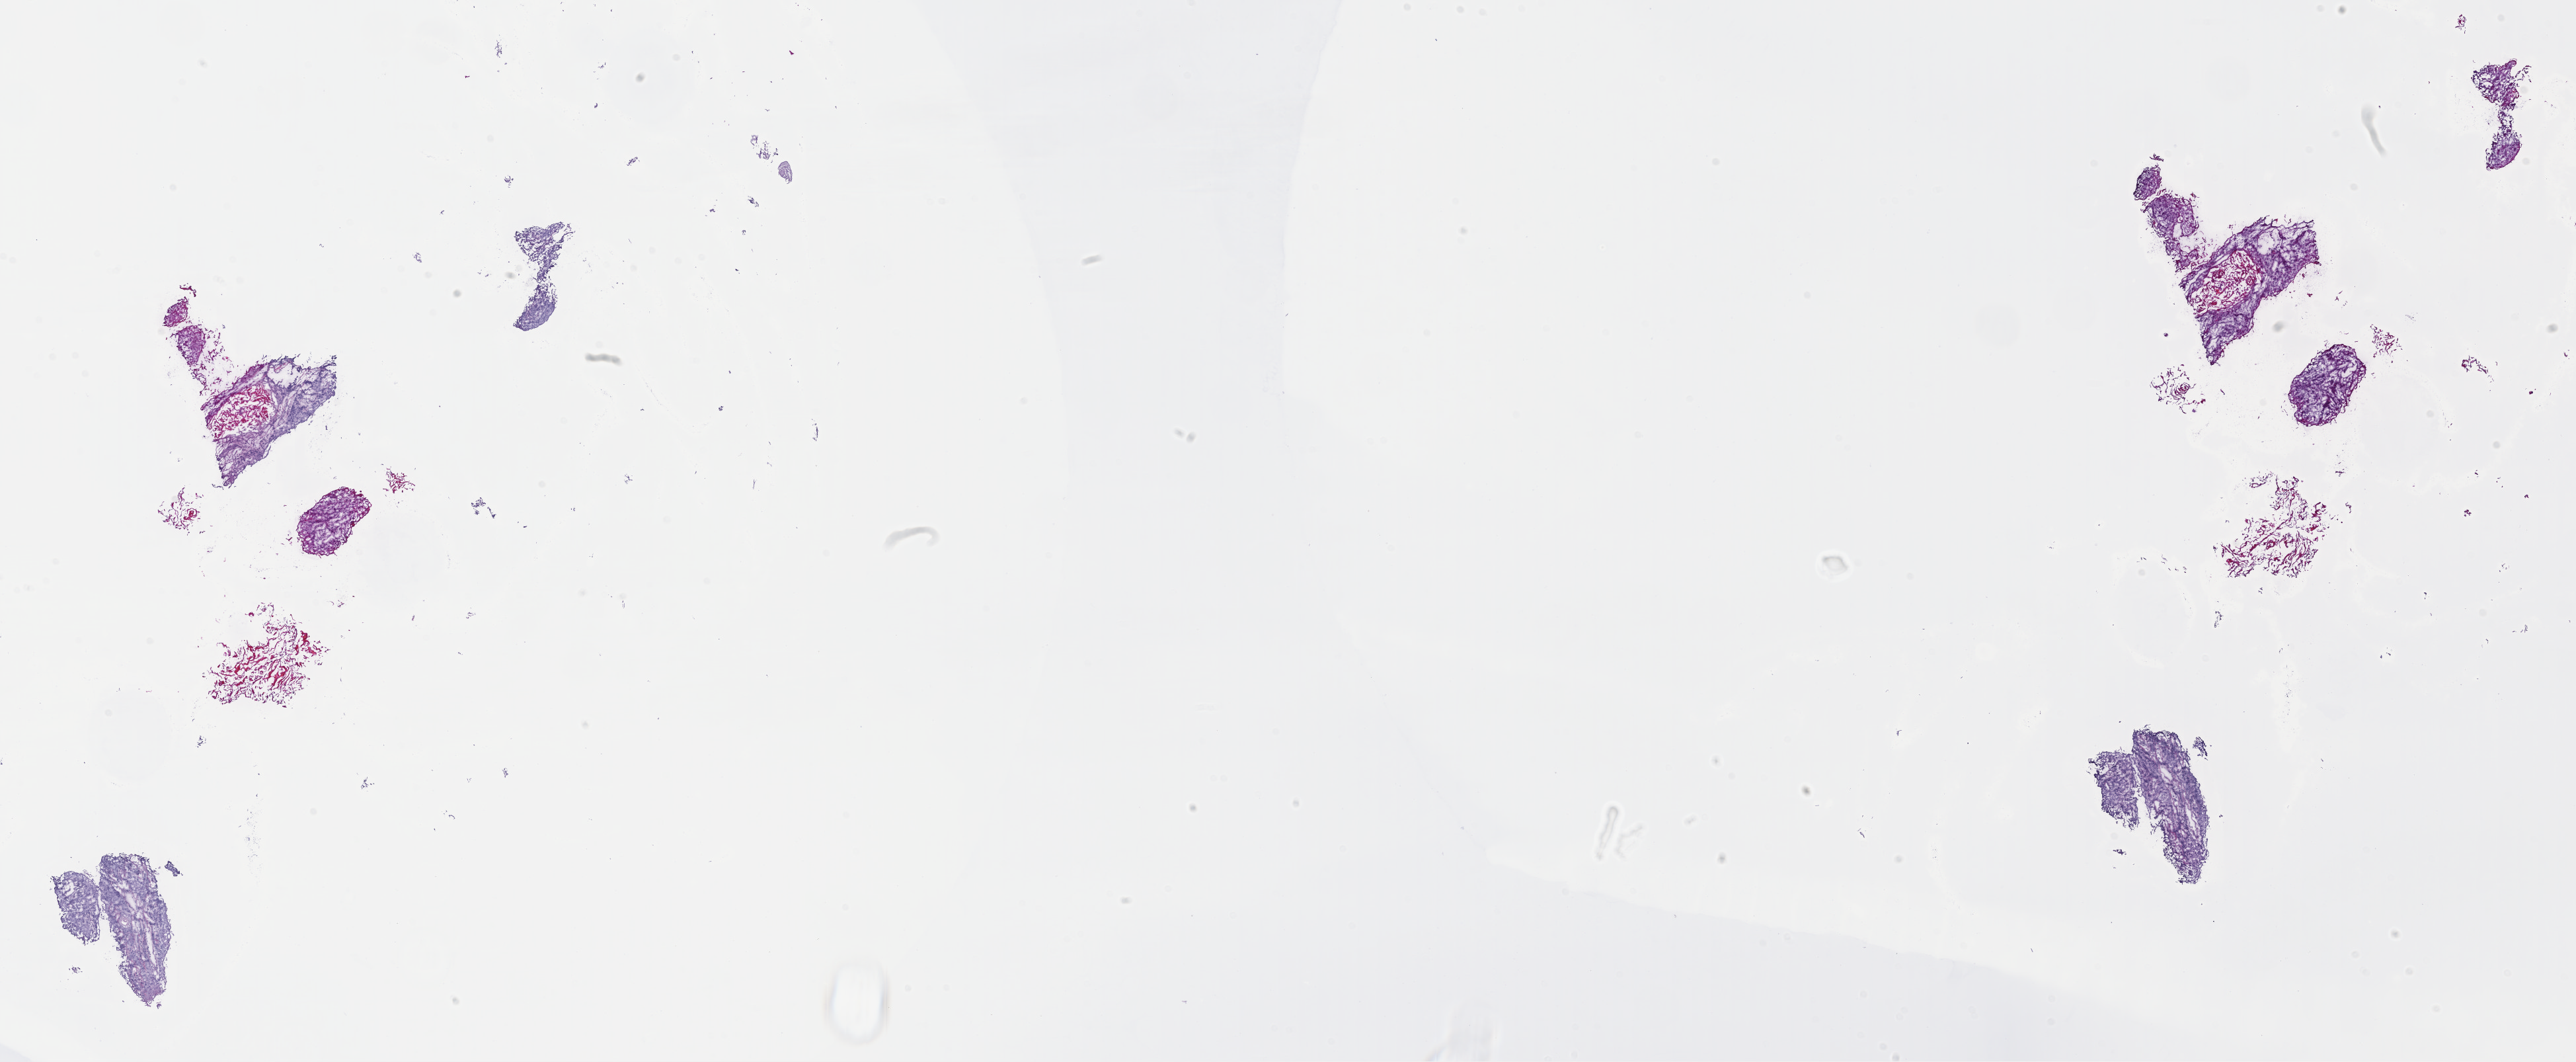
Whole-slide histology image, H&E-stained, a low-resolution overview of the entire scanned area, about 30.6 x 12.6 mm (from a 40x scan). Frozen section from the top of the tissue portion. Primary tumour sample from the head and neck. Male patient; age at initial diagnosis 65 years. Histologic grade: G2 (moderately differentiated). Composition of this section per pathologist review: tumour cells 65%, tumour nuclei 65%, normal cells 0%, stromal cells 20%, necrosis 15%. Infiltration values recorded for this section: lymphocyte infiltration 25%, monocyte infiltration 0%, neutrophil infiltration 3%.
Histologic diagnosis: Squamous cell carcinoma, NOS (larynx, NOS). AJCC pathologic stage: IVA (7th edition).